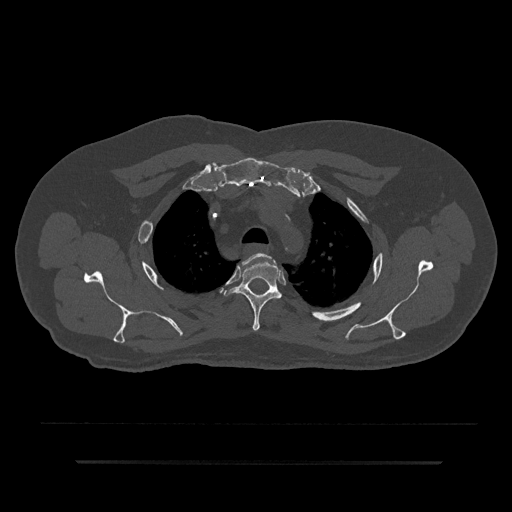
CT including the spine, one axial slice; slice 659 of 797 in the series (ordered by position); reconstruction kernel Br40s/3; 120 kVp; bone window (W 1800 / L 400 HU); 0.5 mm slice thickness; 512 × 512 image matrix, field of view 464 × 464 mm. Patient: male, 59 years. Case-level facts recorded for this patient, not image findings: primary cancer: bile ducts.
Annotated regions visible in this slice (semi-automatic segmentation, software-assisted and operator-edited):
- T2 vertebra: bounding box [x1, y1, x2, y2] px = [238, 253, 272, 266]
- T3 vertebra: [224, 261, 282, 331]